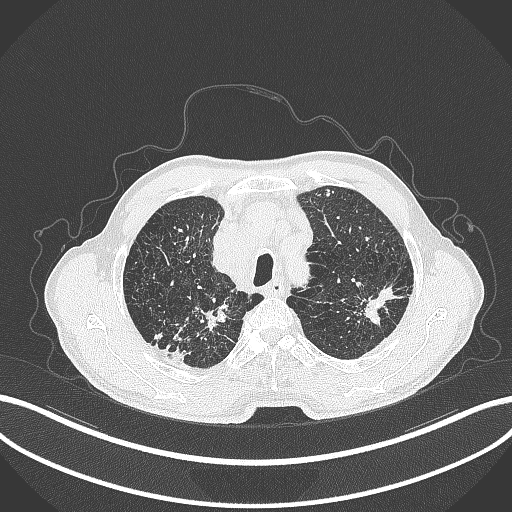
Chest CT, one axial slice; position 364 of 463 along the scan axis; reconstruction kernel B70f; lung window (W 1500 / L -600 HU); 512 × 512 image matrix. Male patient, age 74 years. Case-level facts recorded for this patient, not image findings: clinical TNM (as recorded): T2a N1 M0.
Outlined on this slice (bounding box drawn by a radiologist):
- lung tumour (recorded histology: adenocarcinoma): bounding box <360,278,404,332> (left, top, right, bottom; pixels)